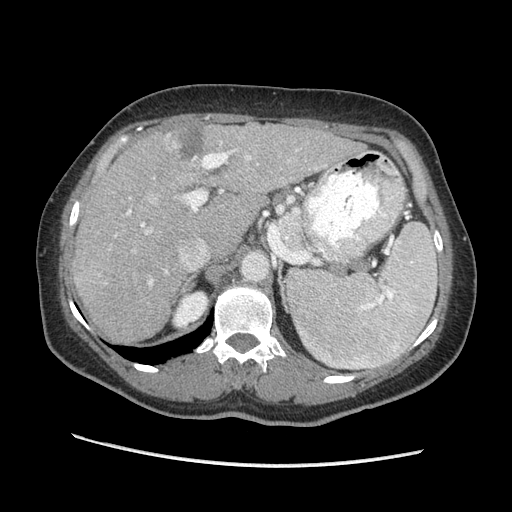
Contrast-enhanced abdominal CT (liver protocol), one axial slice; position 136 of 170 along the scan axis; reconstruction kernel STANDARD; soft-tissue window (W 400 / L 40 HU); 2.5 mm slice thickness; 512 × 512 image matrix, field of view 360 × 360 mm. From the clinical record (not read from this slice): diagnosis: hepatocellular carcinoma (patient treated with transarterial chemoembolisation; whether this scan precedes or follows treatment is not stated here); TNM stage (as recorded): Stage-II; Child-Pugh class: A; tumour differentiation: no biopsy.
Annotated regions visible in this slice (semi-automatically segmented with operator editing):
- liver parenchyma outside the tumour (the mass and vessels are separate outlines, so this box may not span the whole liver): bounding box [x1, y1, x2, y2] px = [72, 122, 366, 342]
- mass: [163, 127, 205, 162]
- liver vessels: [115, 142, 326, 286]